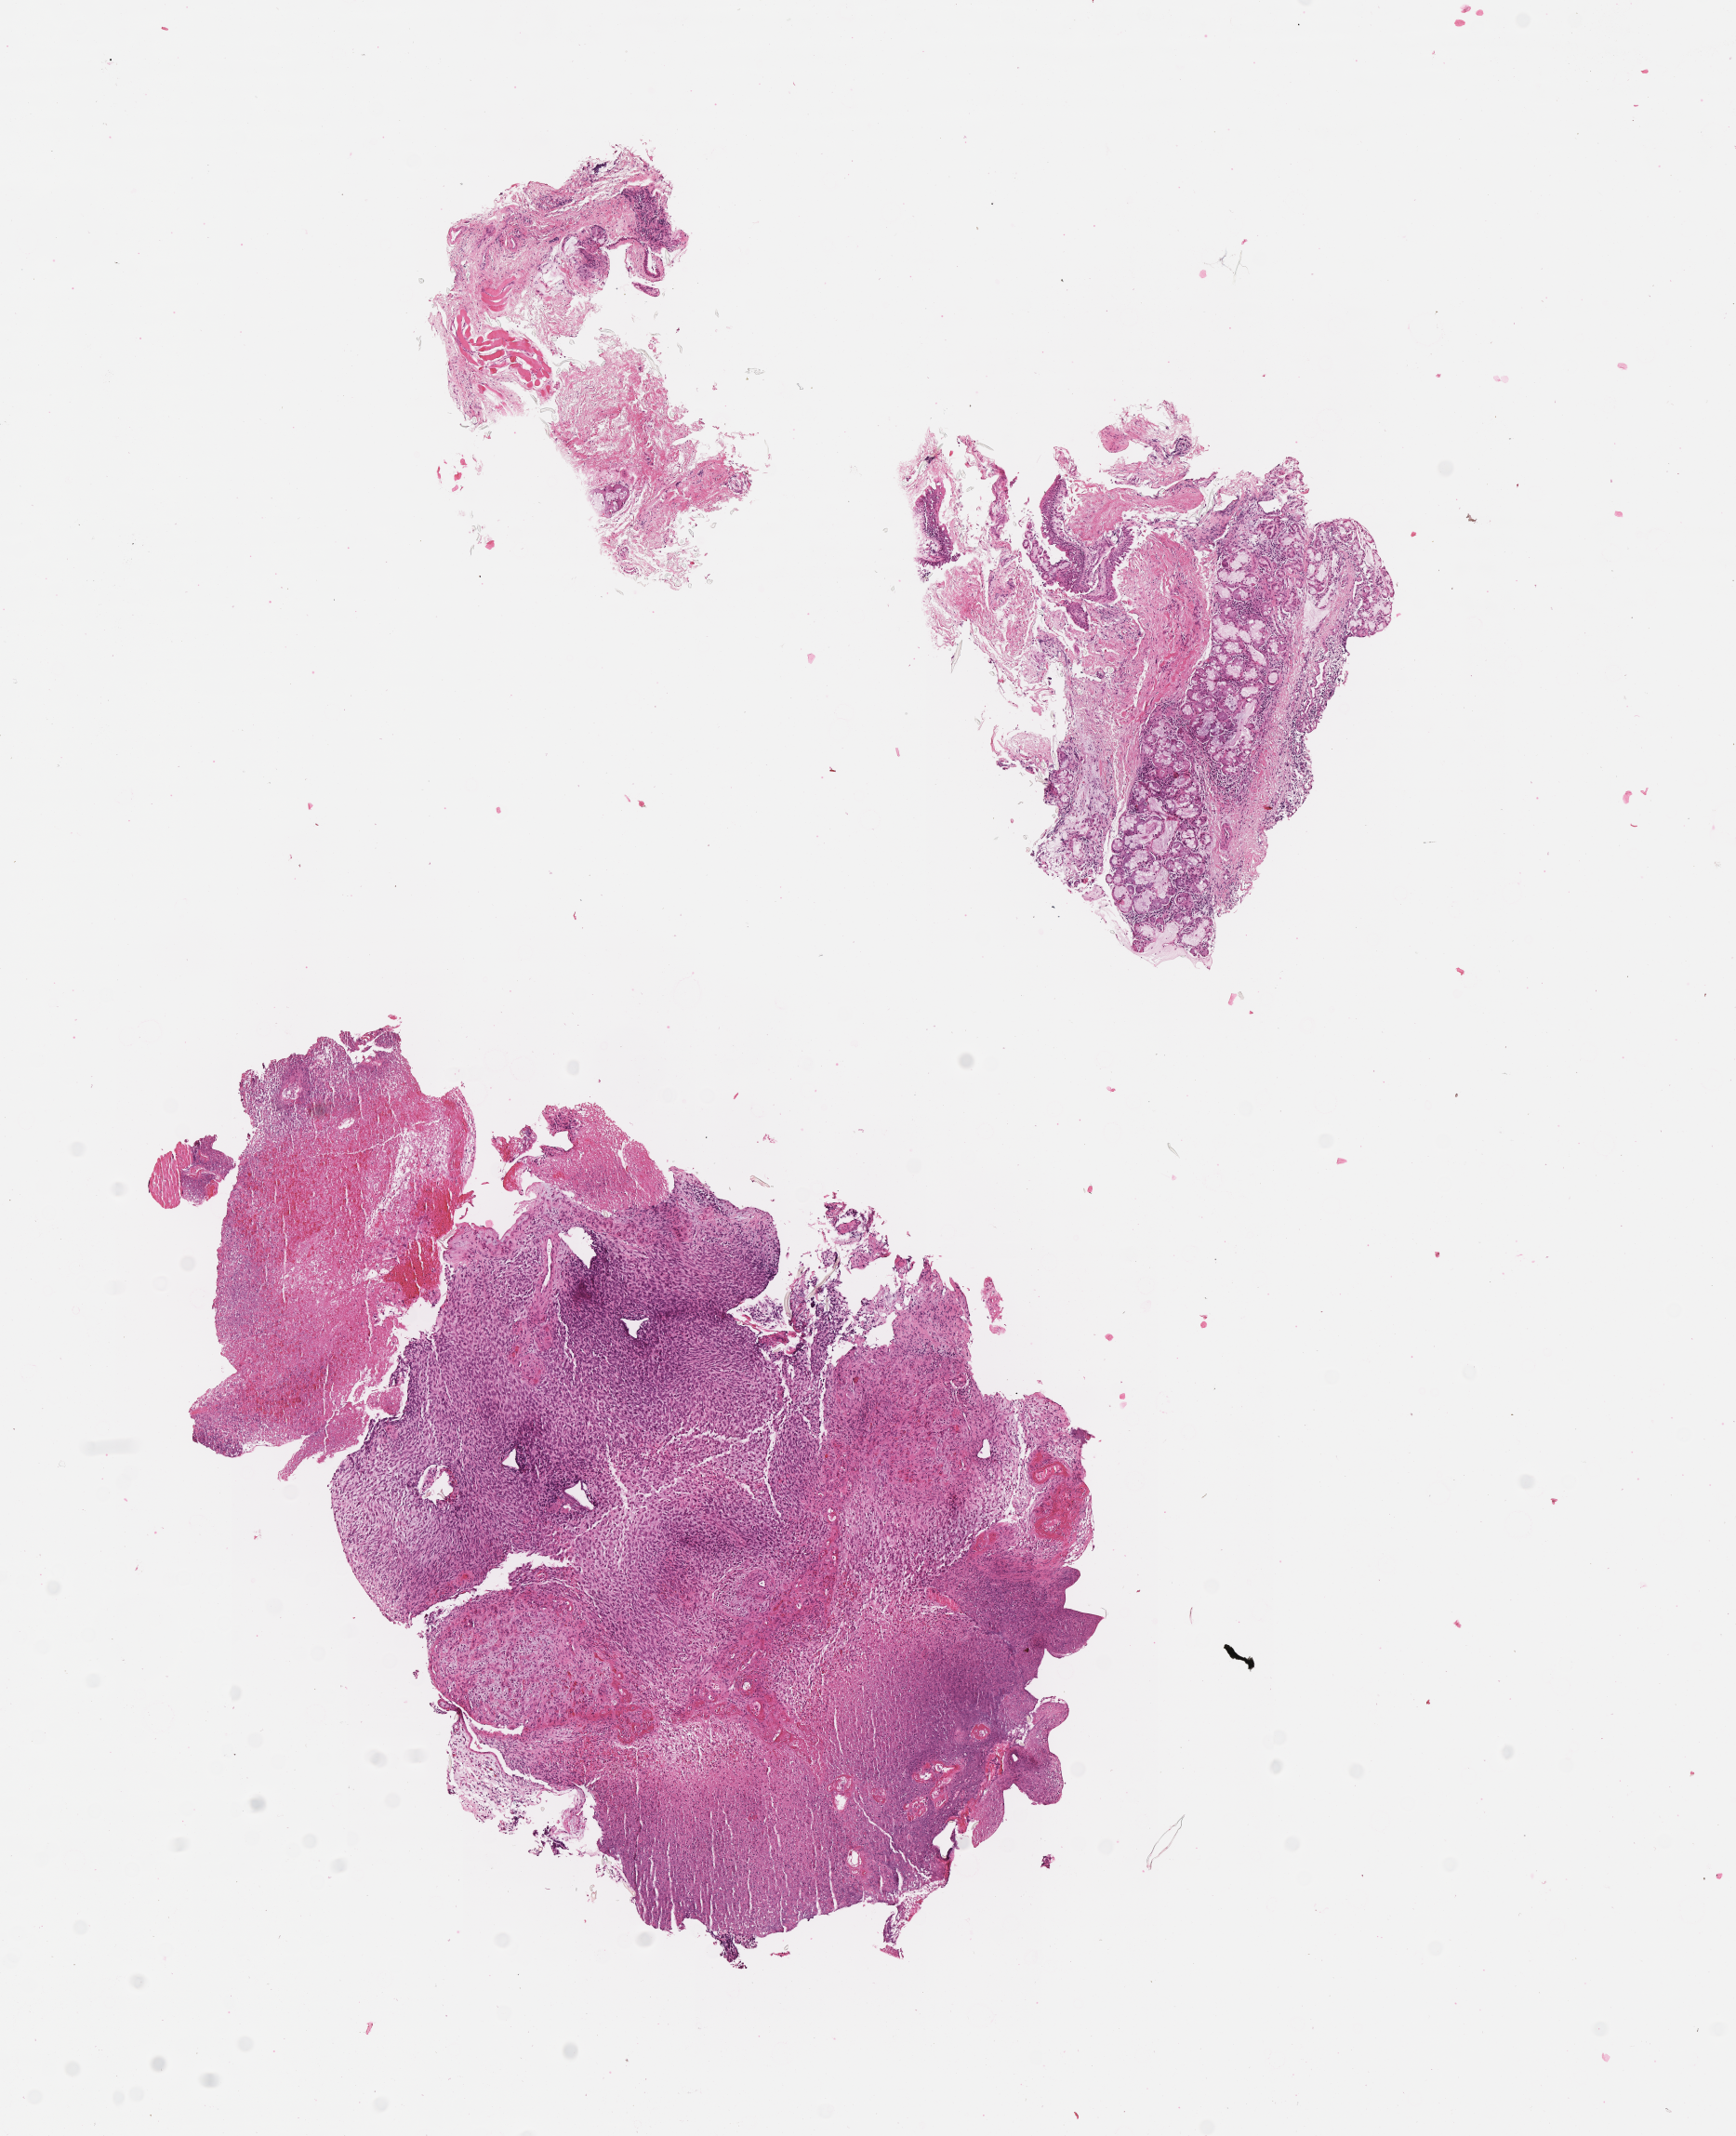
H&E whole-slide image of tumor tissue — a low-resolution overview of the entire scanned area, about 7.5 x 9.3 mm, formalin-fixed paraffin-embedded section, sample anatomic site: nasopharynx-left. Male patient, age at diagnosis 8.3 years.
Diagnosis: rhabdomyosarcoma; histological classification: embryonal rhabdomyosarcoma. Stage (as recorded): 2. Metastatic status at presentation (as recorded): non-metastatic (confirmed).